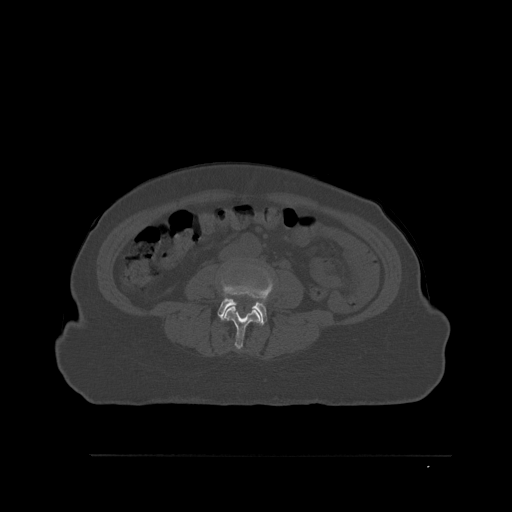
CT including the spine, one axial slice; position 216 of 527 along the scan axis; bone window (W 1800 / L 400 HU); 512 × 512 image matrix. Female patient, age 73 years. Case-level facts recorded for this patient, not image findings: primary cancer: breast.
Structures marked on this image (semi-automatically segmented with operator editing):
- L3 vertebra: bounding box [x1, y1, x2, y2] px = [222, 304, 262, 350]
- L4 vertebra: [217, 268, 274, 325]